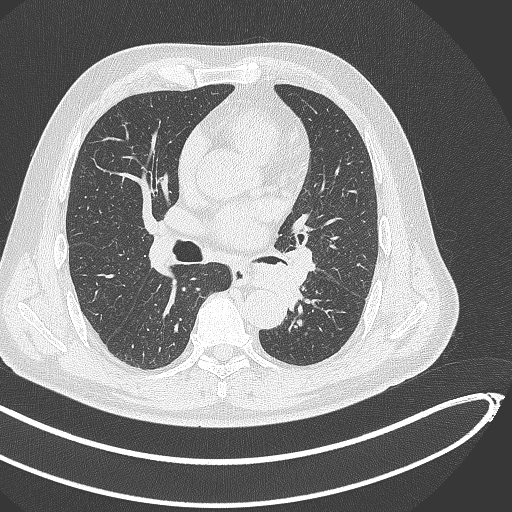
Chest CT, one axial slice. Slice 254 of 468 in the series (ordered by position). Reconstruction kernel B70f. 120 kVp. Lung window (W 1500 / L -600 HU). 1 mm slice thickness. 512 × 512 image matrix, field of view 400 × 400 mm. Male patient, age 64 years. From the clinical record (not read from this slice): clinical TNM (as recorded): T1c N0 M0.
Annotated regions visible in this slice (bounding box drawn by a radiologist):
- lung tumour (recorded histology: squamous cell carcinoma): box from (x=248, y=262) to (x=310, y=321) px